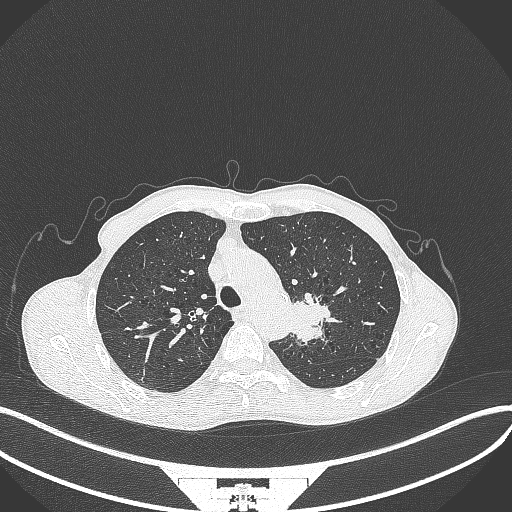
Chest CT, one axial slice; slice 312 of 386 in the series (ordered by position); reconstruction kernel B70f; 120 kVp; lung window (W 1500 / L -600 HU); 1 mm slice thickness; 512 × 512 image matrix, field of view 400 × 400 mm. Patient: male, 65 years. Case-level facts recorded for this patient, not image findings: clinical TNM (as recorded): T2b N0 M0.
Annotated regions visible in this slice (bounding box drawn by a radiologist):
- lung tumour (recorded histology: adenocarcinoma): bounding box <294,289,337,347> (left, top, right, bottom; pixels)